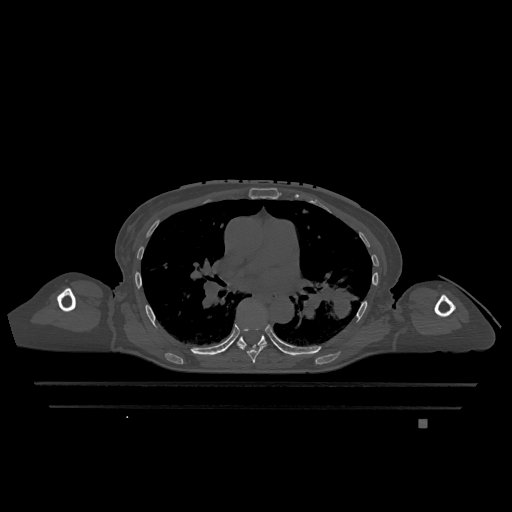
CT including the spine, one axial slice; slice 765 of 1317 in the series (ordered by position); bone window (W 1800 / L 400 HU); 0.5 mm slice thickness; 512 × 512 image matrix, field of view 500 × 500 mm. Female patient, age 74 years. From the clinical record (not read from this slice): primary cancer: lung.
Structures marked on this image (semi-automatically segmented with operator editing):
- T6 vertebra: bounding box <239,328,266,363> (left, top, right, bottom; pixels)
- T7 vertebra: <237,329,267,347>